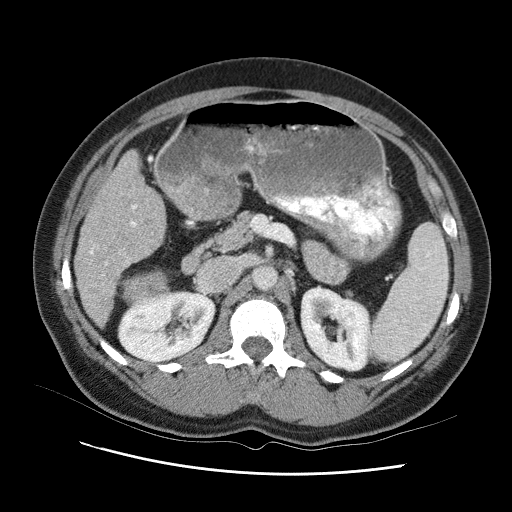
Contrast-enhanced abdominal CT (liver protocol), one axial slice; position 41 of 95 along the scan axis; reconstruction kernel STANDARD; one of 2 acquisitions stored at this slice position; soft-tissue window (W 400 / L 40 HU); 2.5 mm slice thickness; 512 × 512 image matrix, field of view 360 × 360 mm. From the clinical record (not read from this slice): diagnosis: hepatocellular carcinoma (patient treated with transarterial chemoembolisation; whether this scan precedes or follows treatment is not stated here); TNM stage (as recorded): Stage-I; Child-Pugh class: B; tumour differentiation: moderately differentiated.
Structures marked on this image (semi-automatic segmentation, software-assisted and operator-edited):
- liver parenchyma outside the tumour (the mass and vessels are separate outlines, so this box may not span the whole liver): bounding box <74,138,178,336> (left, top, right, bottom; pixels)
- mass: <110,250,181,307>
- liver vessels: <96,173,144,322>